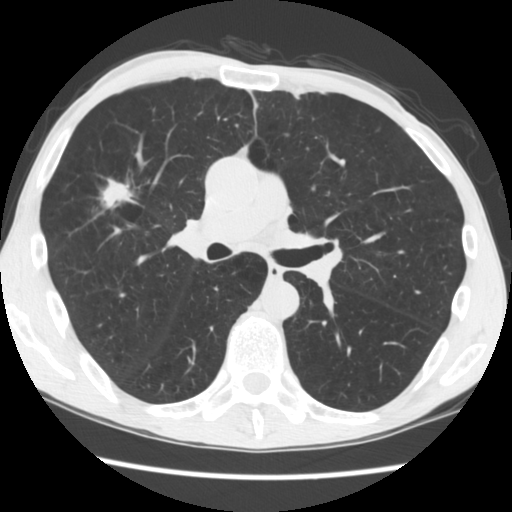
Axial slice from a low-dose chest CT screening exam, second annual screen, lung window (W 1500 / L -600 HU), 2.5 mm slice thickness, 512 × 512 image matrix. Male participant, aged 56 years at enrolment. Current smoker at enrolment.
Expert-annotated lung lesion, box from (x=90, y=170) to (x=147, y=231) px. The screening reader recorded 2 non-calcified nodules or masses ≥4 mm on this exam (right upper lobe, left upper lobe); which of them this box marks is not recorded.